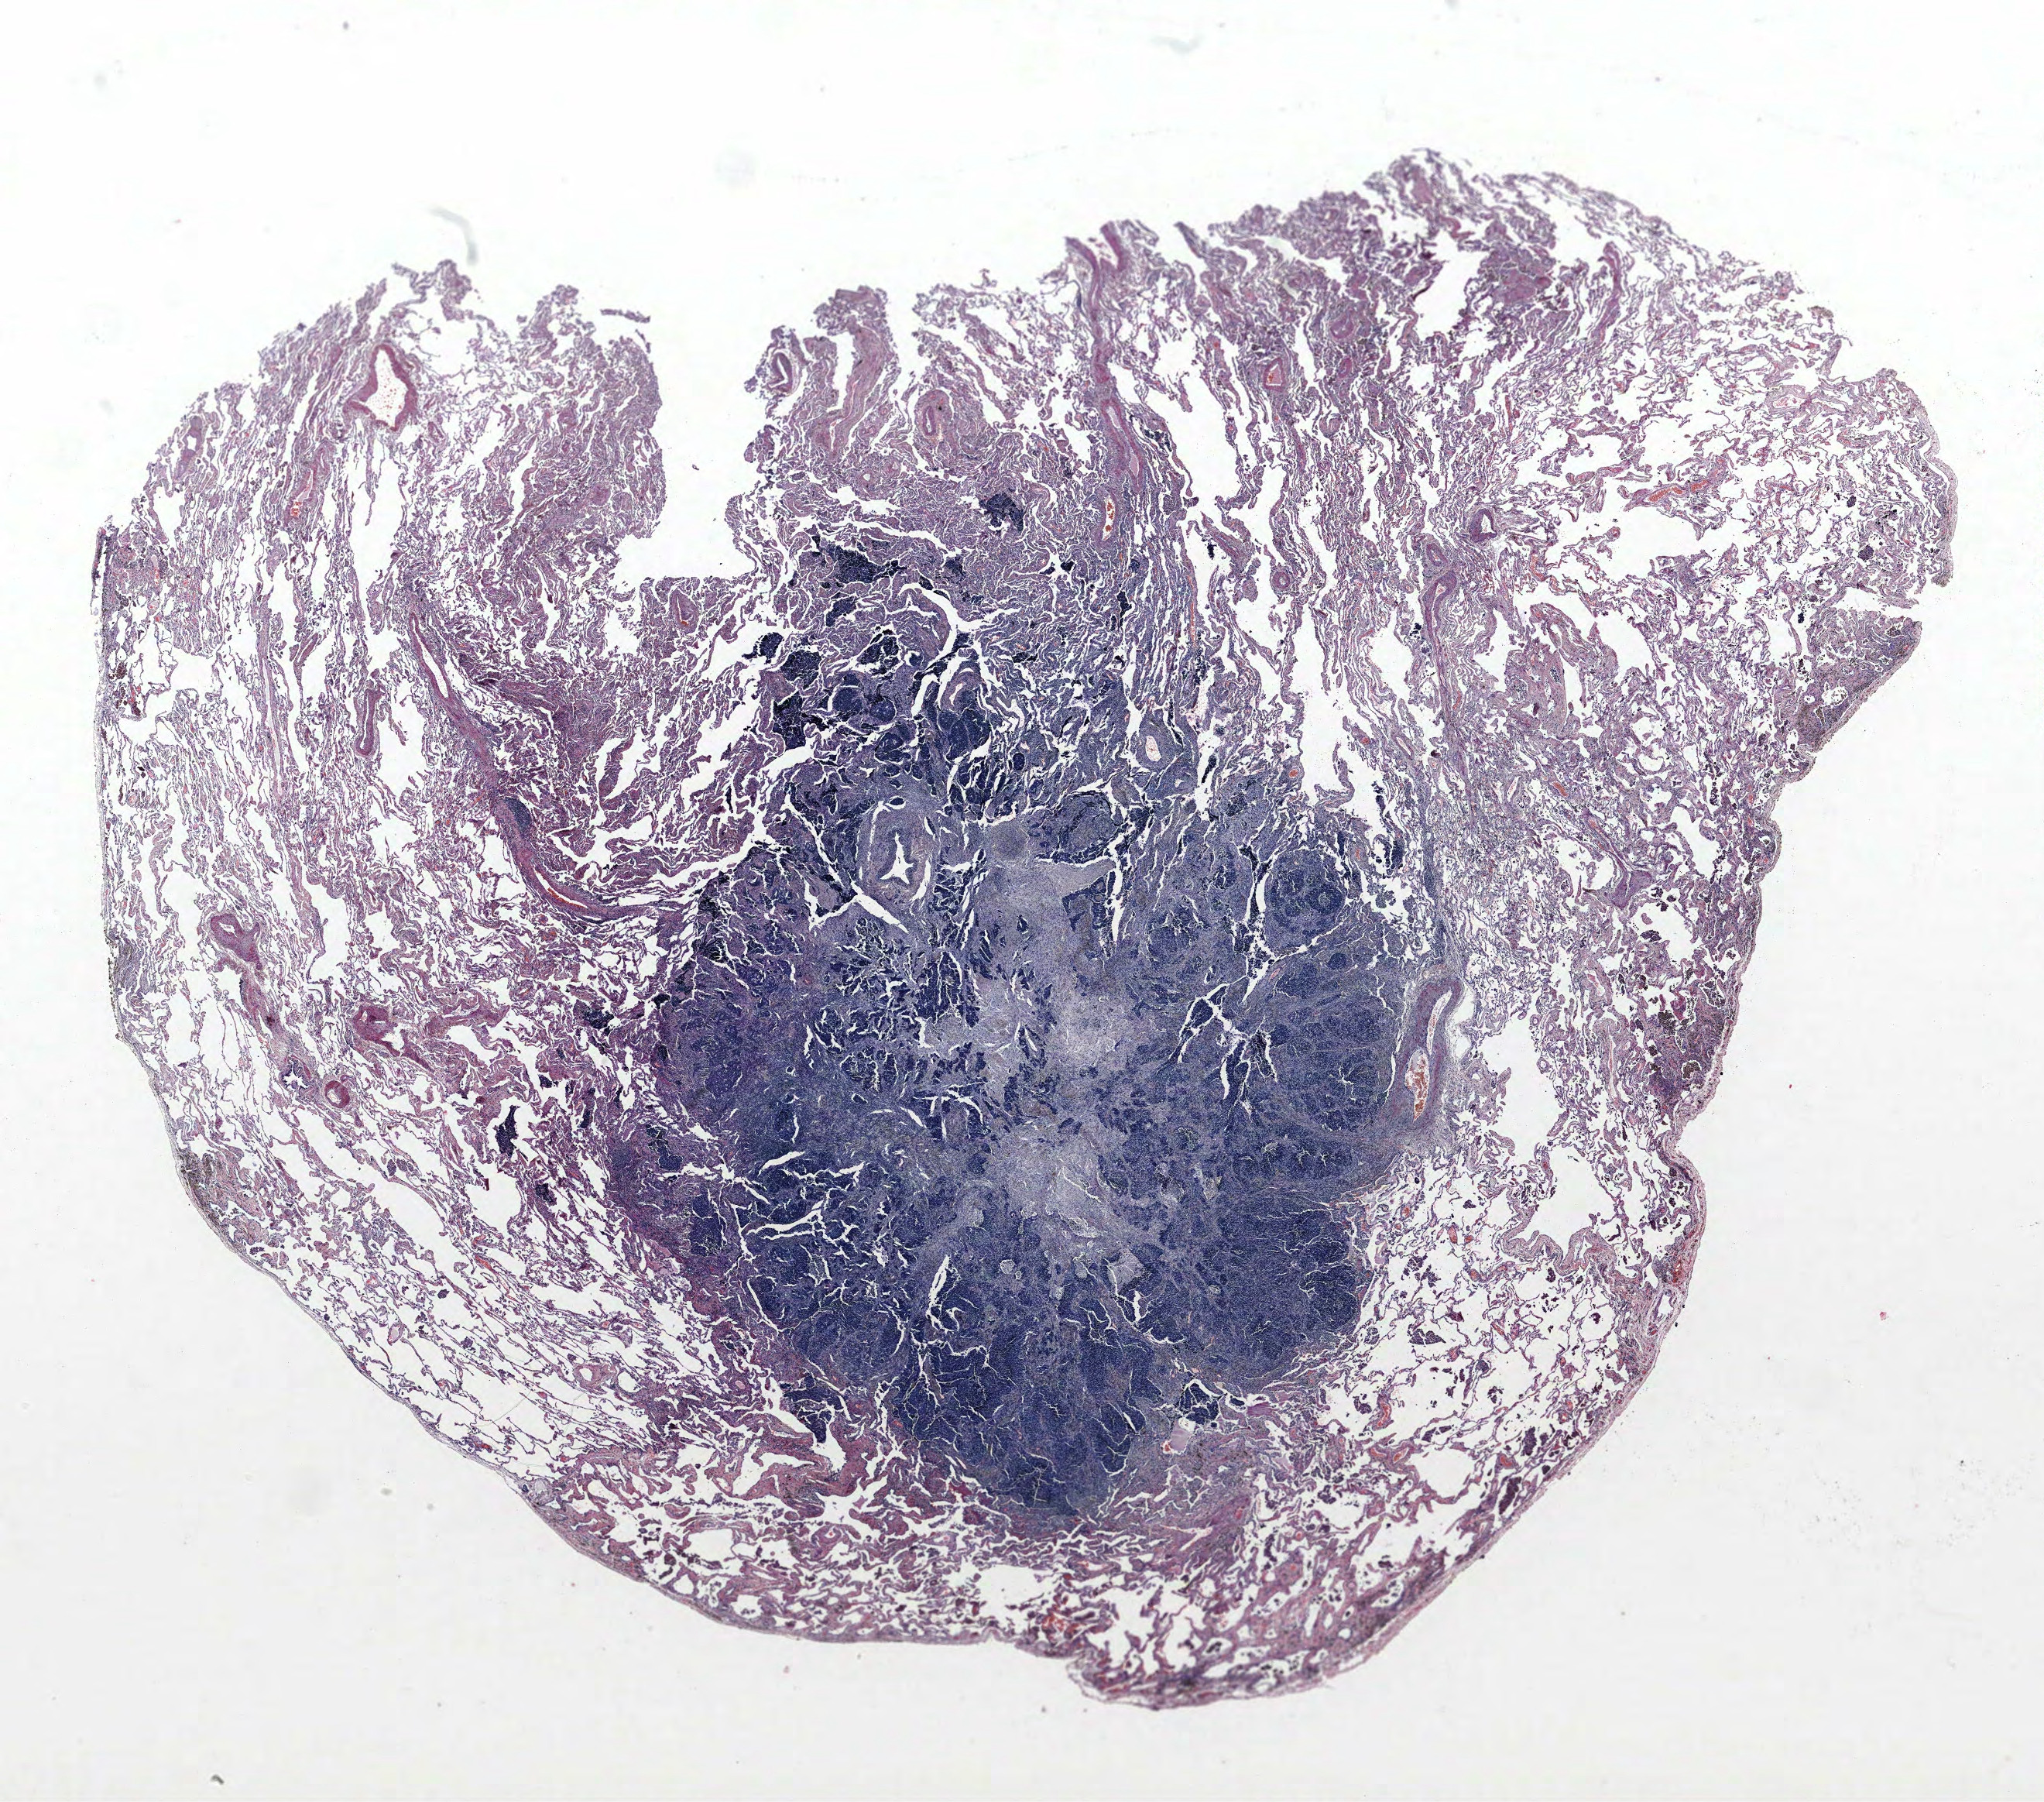
Whole-slide histology image, H&E-stained — shown as a low-resolution overview of the whole scanned area (about 21.1 x 18.6 mm); formalin-fixed paraffin-embedded (FFPE) section; lung tissue. Male patient, aged 64 at enrolment. Grade: poorly differentiated (G3).
* tumour size (pathology): 11 mm
* primary tumour location (clinical record): left upper lobe
* stage (AJCC 6th edition): IIIA
* participant's lung-cancer diagnosis: Neuroendocrine carcinoma, NOS